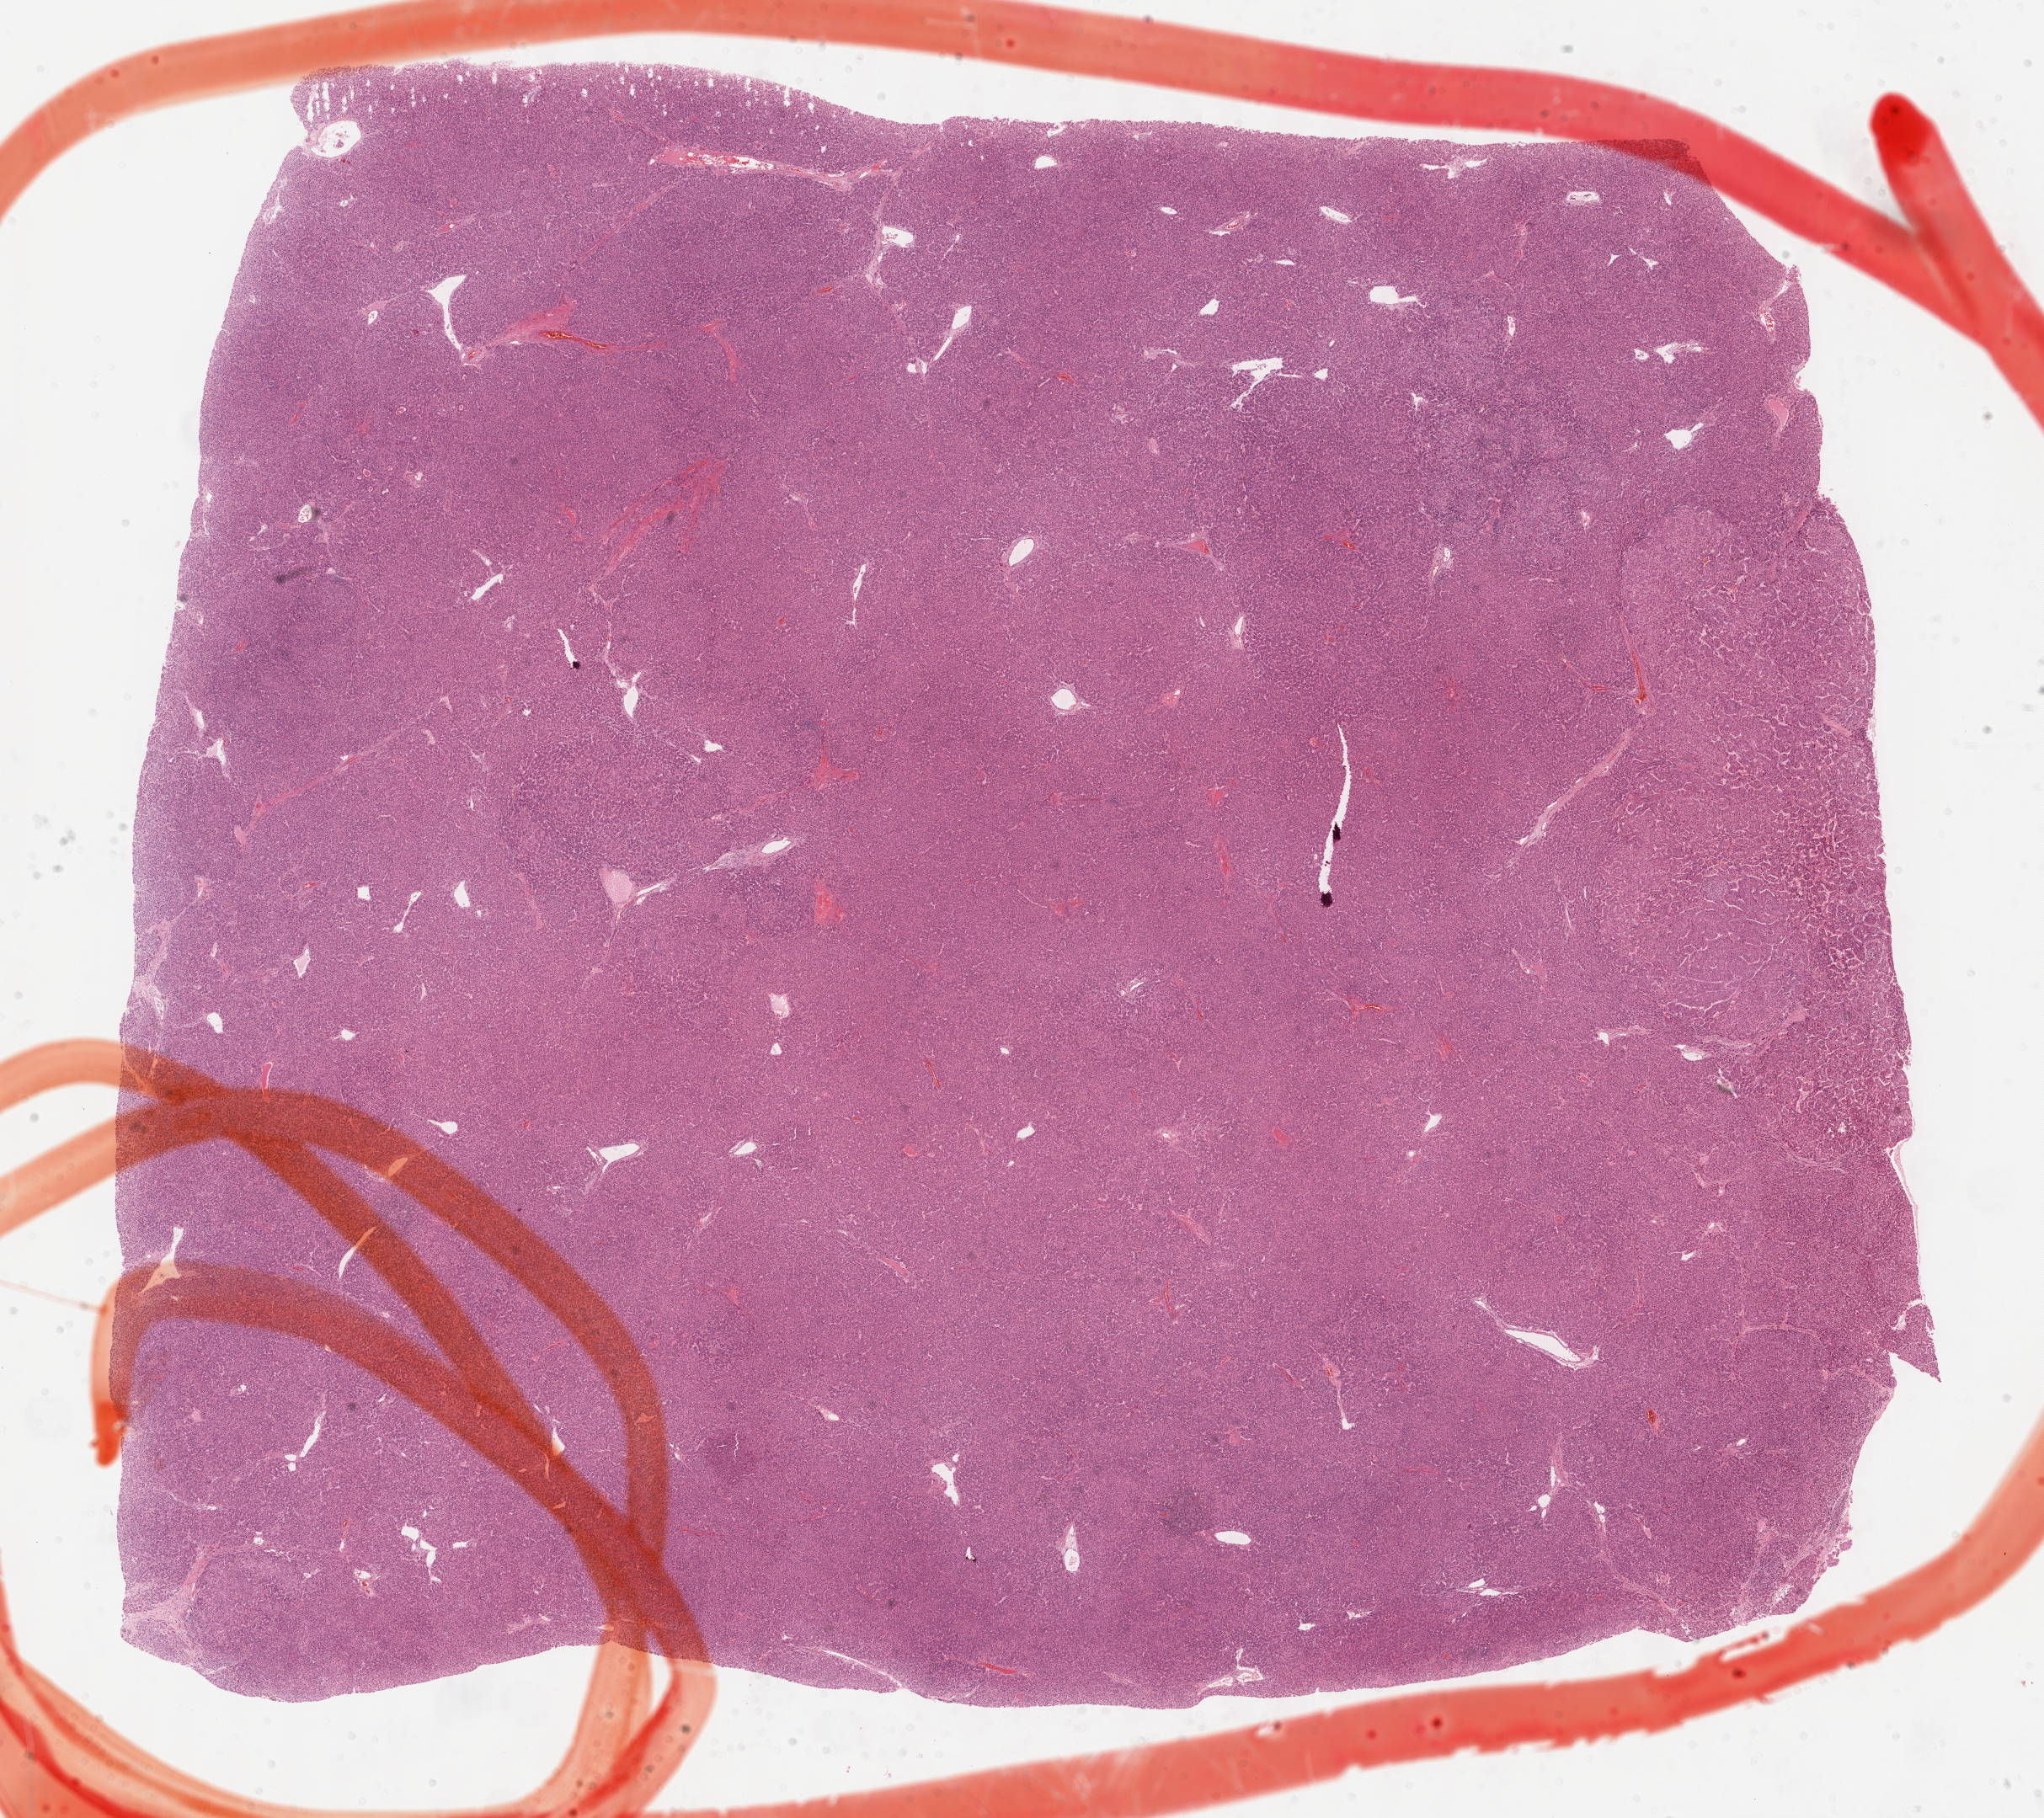
H&E whole-slide image, whole scanned area (about 19.6 x 17.5 mm) shown as a low-resolution overview; formalin-fixed paraffin-embedded (FFPE) diagnostic section; liver, primary tumour sample. Female, age 20 years at initial diagnosis. Histologic grade: G3 (poorly differentiated).
AJCC pathologic stage: II. Diagnosis: Hepatocellular carcinoma, NOS.